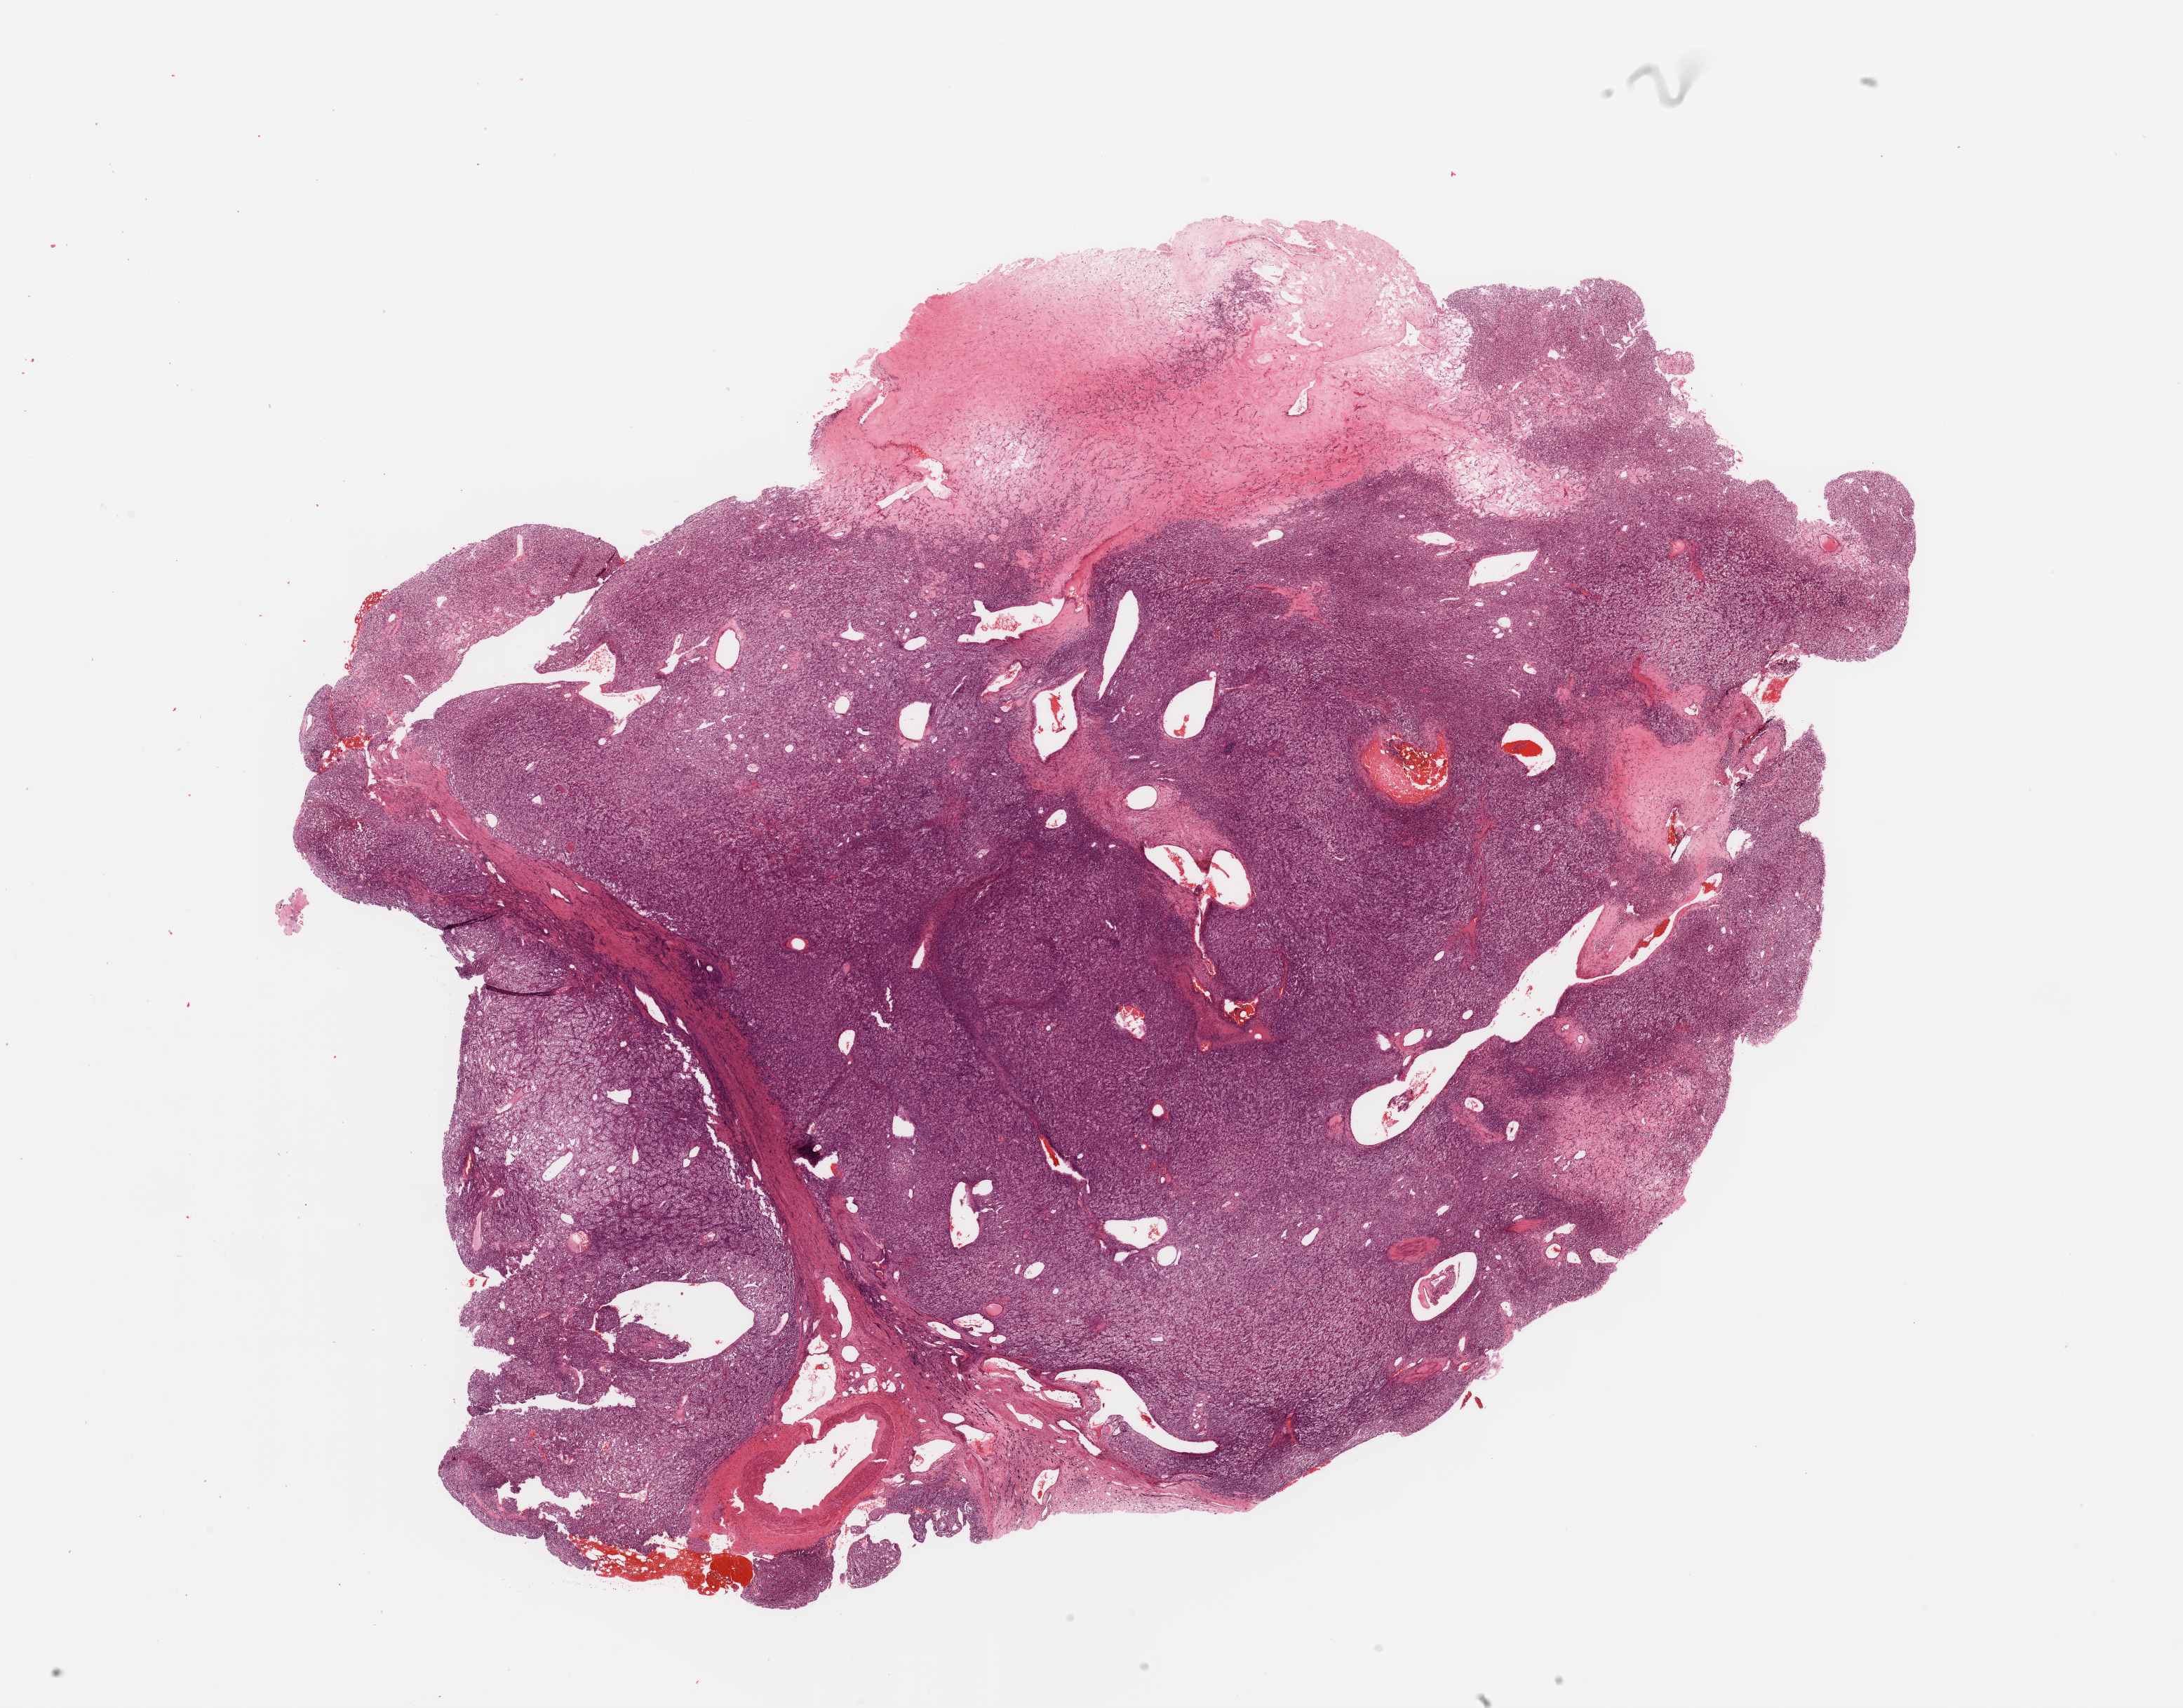
Whole-slide histology image, H&E-stained — whole scanned area (about 24.6 x 19.3 mm, slide scanned at 20x) shown as a low-resolution overview; tumour tissue sample, kidney. Male, 63 y/o. Histologic grade: G1 (well differentiated).
Diagnosis: Renal cell carcinoma, NOS.